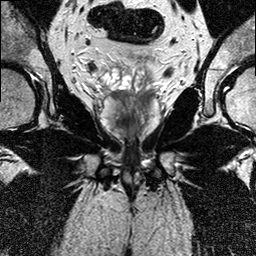
Multiparametric prostate MRI examination; 2 images, each a single mid-volume slice chosen by position (not for content). Treatment context recorded for this patient: Surgery.
Image 1: T2-weighted coronal slice, series "T2W_TSE_COR", slice 14 of 26, 3 mm slice thickness.
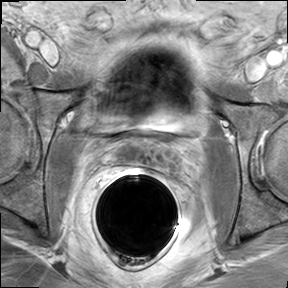
Image 2: DCE (dynamic gadolinium-enhanced) axial slice, series "AX BLISS_GAD_8", slice 18 of 34, dynamic phase 5 of 8, 6 mm slice thickness.
Report of this MRI examination:
prostate has a maximal lateral diameter of 4.6 cm, a maximal craniocaudal diameter of 3.7 cm and a maximal AP diameter of 2.2 cm resulting in an estimated gland volume of 20 cc. The zonal anatomy is preserved. In the midthird and apical third the prostate there are geographic areas of low signal on the T2-weighted images in the posterior aspects of the peripheral zones of both side between 5:00 and 8:00. The dominant area measures 18 x 6 mm and is located in the midthird paramedian right between 6 and 8:00 and extents into the apical third. This area shows also suspicious kinetics on the dynamic series.The area abuts the "pseudo-capsule" posterior and posterior lateral. However, there is NO evidence for involvement of the neurovascular bundle on either side. No evidence for seminal vesicles infiltration. No evidence of involvement of bladder neck and rectal wall. No suspiciously enlarged obturator and iliac lymph nodes; several up to 7 x 4 mm obturator lymph nodes seen, on both sides. IMPRESSION: 1) Bilateral tumor, predominantly on the right within the posterior and posterior lateral peripheral zones between 5 and 8 o'clock, in mid third and apical third of the prostate, as detailed above (significant images are annotated on PACS). 2) No evidence of extraprostatic disease - specifically no evidence of extension into the neuro-vascular bundles of either side.

Prostatectomy specimen pathology (as recorded; the surgery followed this MRI):
A: LEFT OBTURATOR LYMPH NODE POCKET B: RIGHT OBTURATOR LYMPH NODE POCKET C: PROSTATE AND SEMINAL VESICLES Final Diagnosis A. LEFT OBTURATOR LYMPH NODE POCKET: FOUR (4) REACTIVE LYMPH NODES, NO TUMOR IDENTIFIED. B. RIGHT OBTURATOR LYMPH NODE POCKET: FOUR (4) REACTIVE LYMPH NODES, NO TUMOR IDENTIFIED. C. PROSTATE AND SEMINAL VESICLES: Procedure: Radical prostatectomy Prostate Size: 3.5x3x2.6cm Weight: 30.6g Lymph Node Sampling: Pelvic lymph node dissection Histologic Type: Adenocarcinoma (acinar, not otherwise specified) Histologic Grade: Gleason grade 3+3 score = 6/10 Primary pattern: Grade 3 Secondary pattern: Grade 3 Tumor Quantitation: Proportion (percentage) of prostate involved by tumor: 15% Extraprostatic Extension: Not identified Seminal Vesicle Invasion: Not identified Margins: Margins uninvolved by invasive carcinoma Treatment Effect on Carcinoma: Not identified Lymph-Vascular Invasion: Not identified Perineural Invasion: Present Additional Pathologic Findings: High-grade prostatic intraepithelial neoplasia (PIN) and chronic inflammation Pathologic Staging (pTNM) Primary Tumor (pT) pT2c: Bilateral disease Regional Lymph Nodes (pN) pN0: No regional lymph nodes metastasis Specify: Number examined: 8 Number involved: 0 Distant Metastasis (pM) Pathologic Stage: (pT2c, pN0)